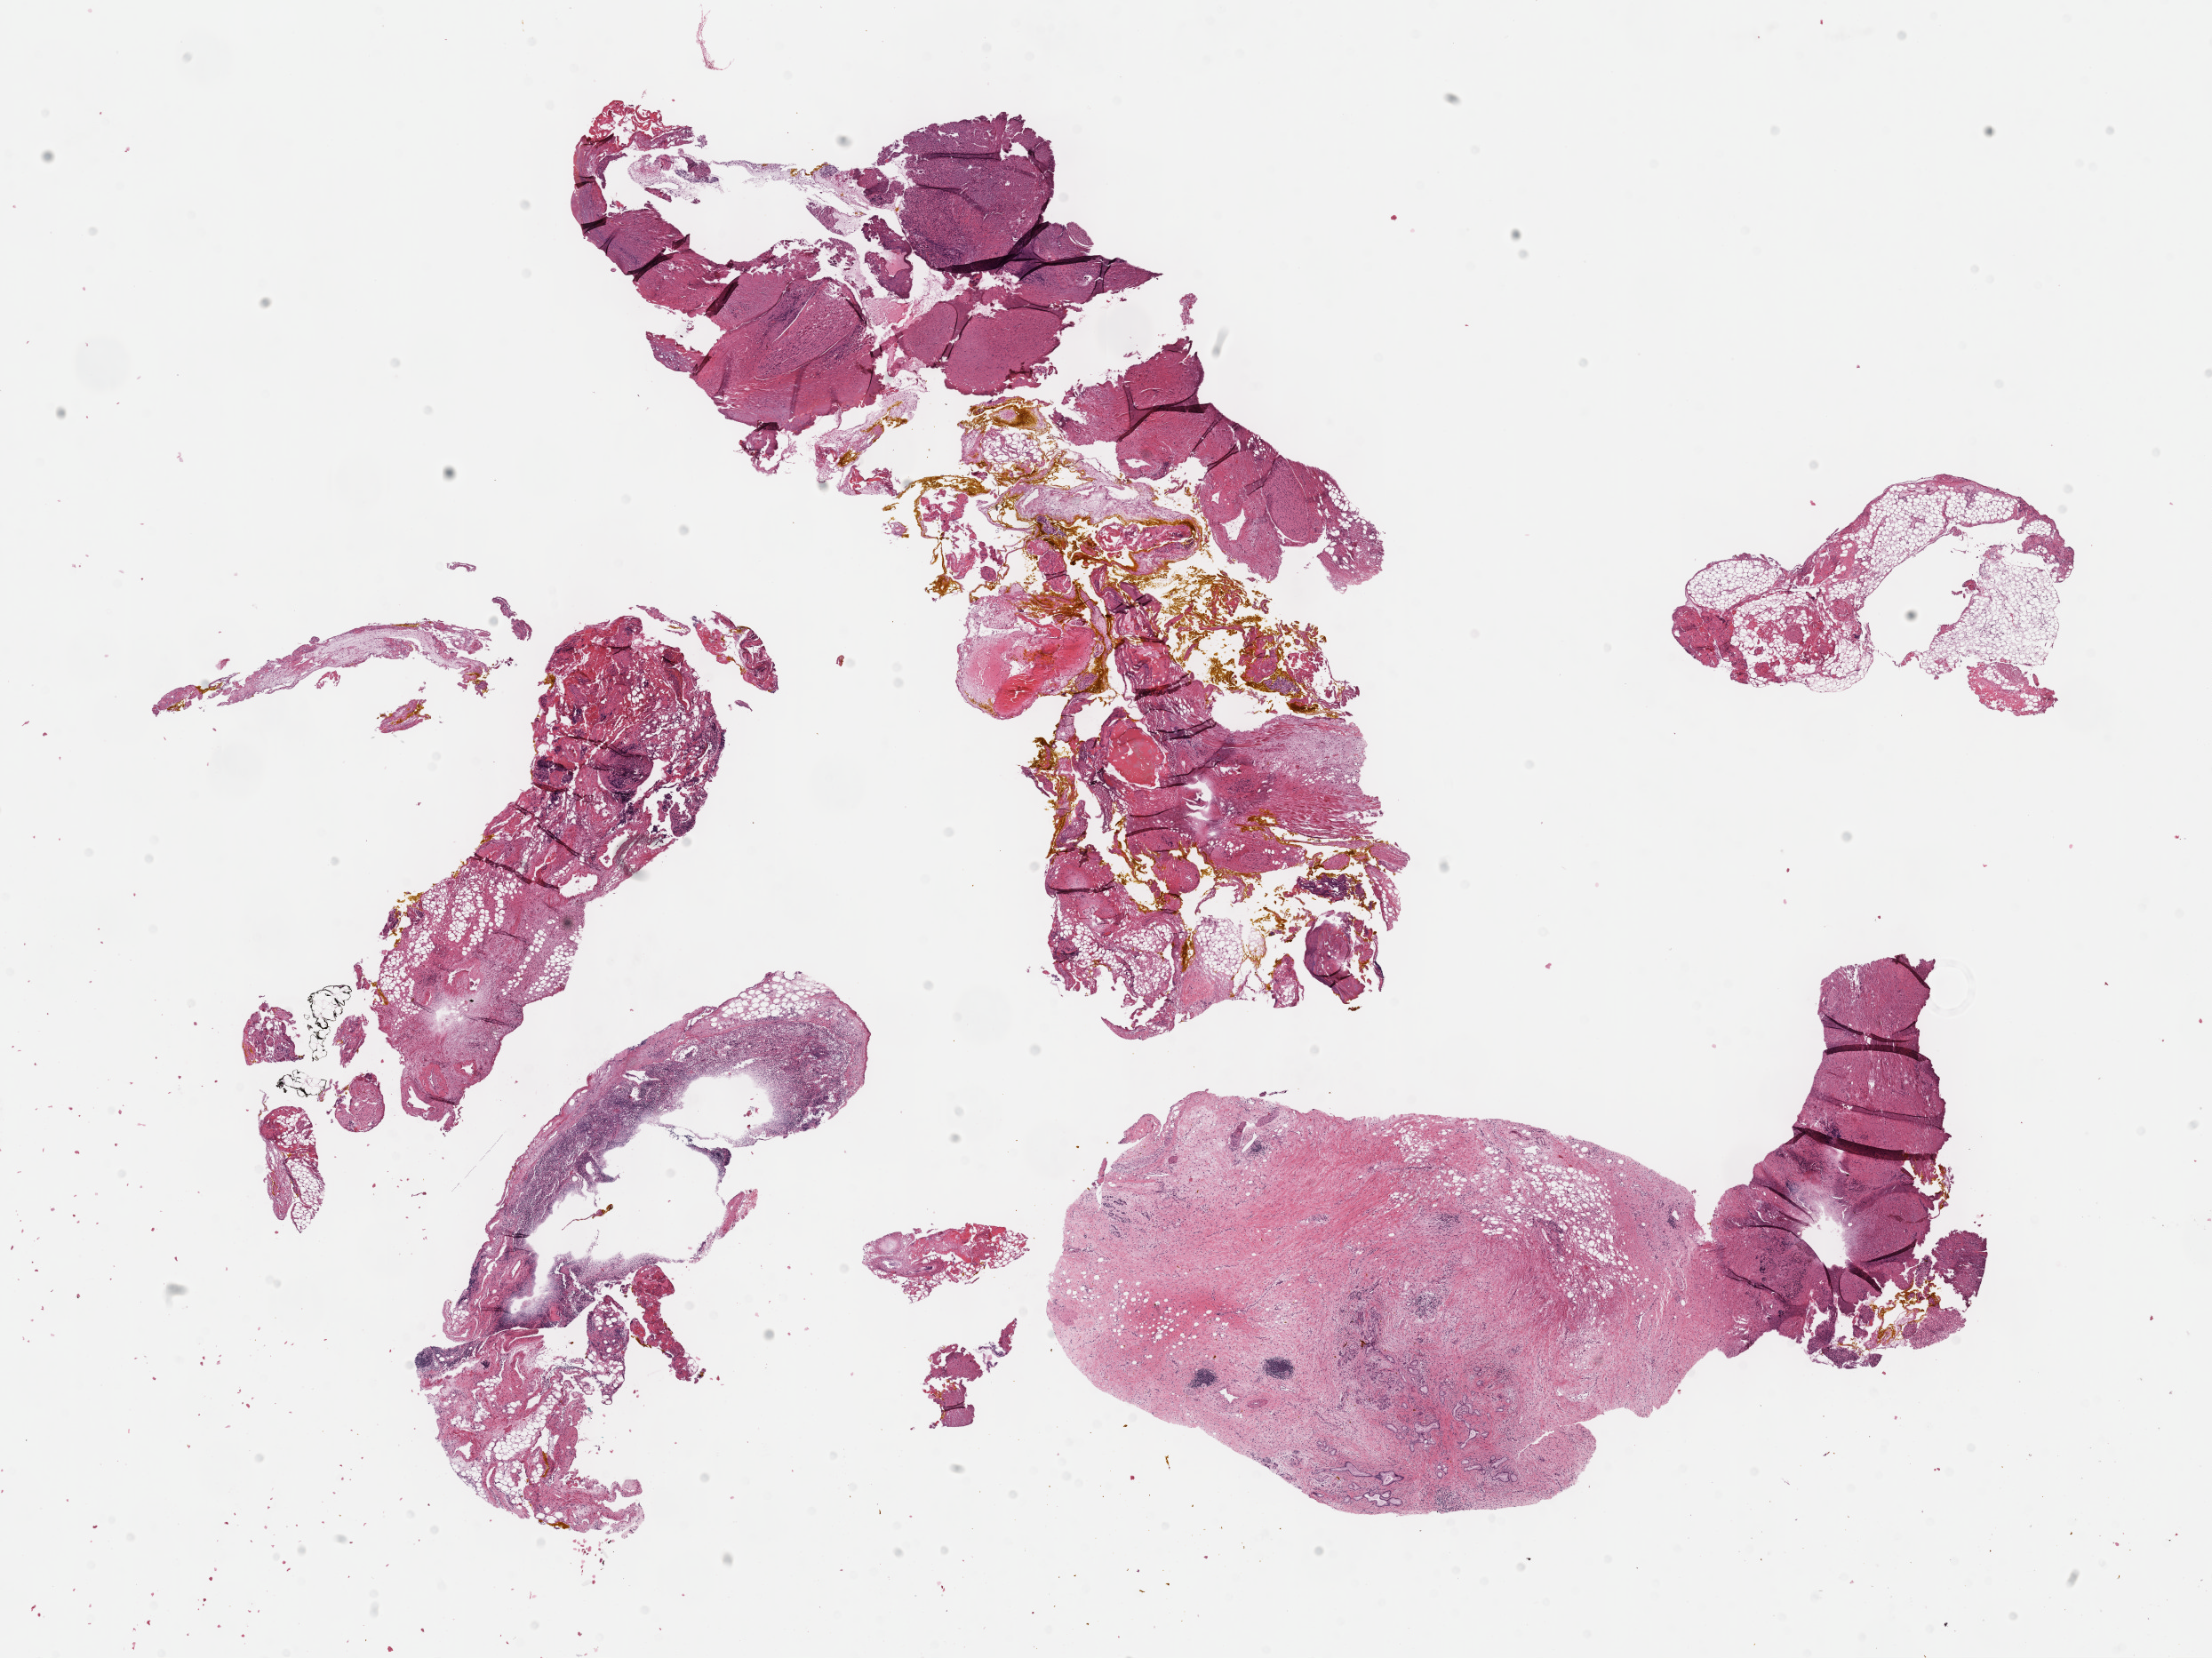
Whole-slide histology image, H&E-stained, whole scanned area (about 20.1 x 15.1 mm) shown as a low-resolution overview. Formalin-fixed paraffin-embedded (FFPE) diagnostic section. Primary tumour sample from the pancreas. Male, age 55 years at initial diagnosis. Histologic grade: G2 (moderately differentiated).
- TNM: T3 N1 M0
- AJCC pathologic stage: IIB (7th edition)
- lymph nodes positive (case pathology): 2 of 22 examined
- pathologic diagnosis: Infiltrating duct carcinoma, NOS (head of pancreas)